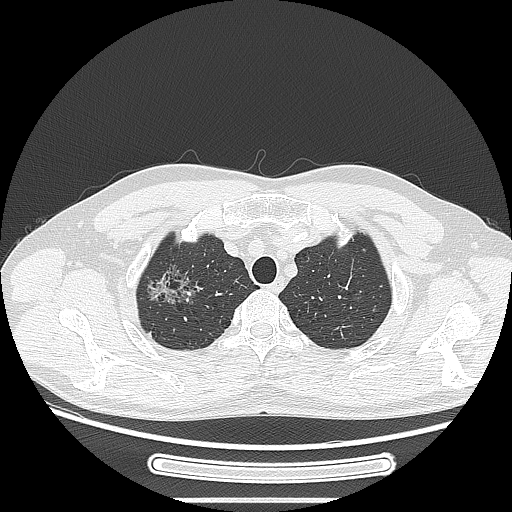
Chest CT, one axial slice. Position 226 of 269 along the scan axis. 120 kVp. Lung window (W 1500 / L -600 HU). 1.25 mm slice thickness. 512 × 512 image matrix, field of view 382 × 382 mm. Male patient, age 53 years. Case-level facts recorded for this patient, not image findings: clinical TNM (as recorded): T1c N0 M0.
Outlined on this slice (bounding box drawn by a radiologist):
- lung tumour (recorded histology: adenocarcinoma): bounding box <133,257,200,319> (left, top, right, bottom; pixels)